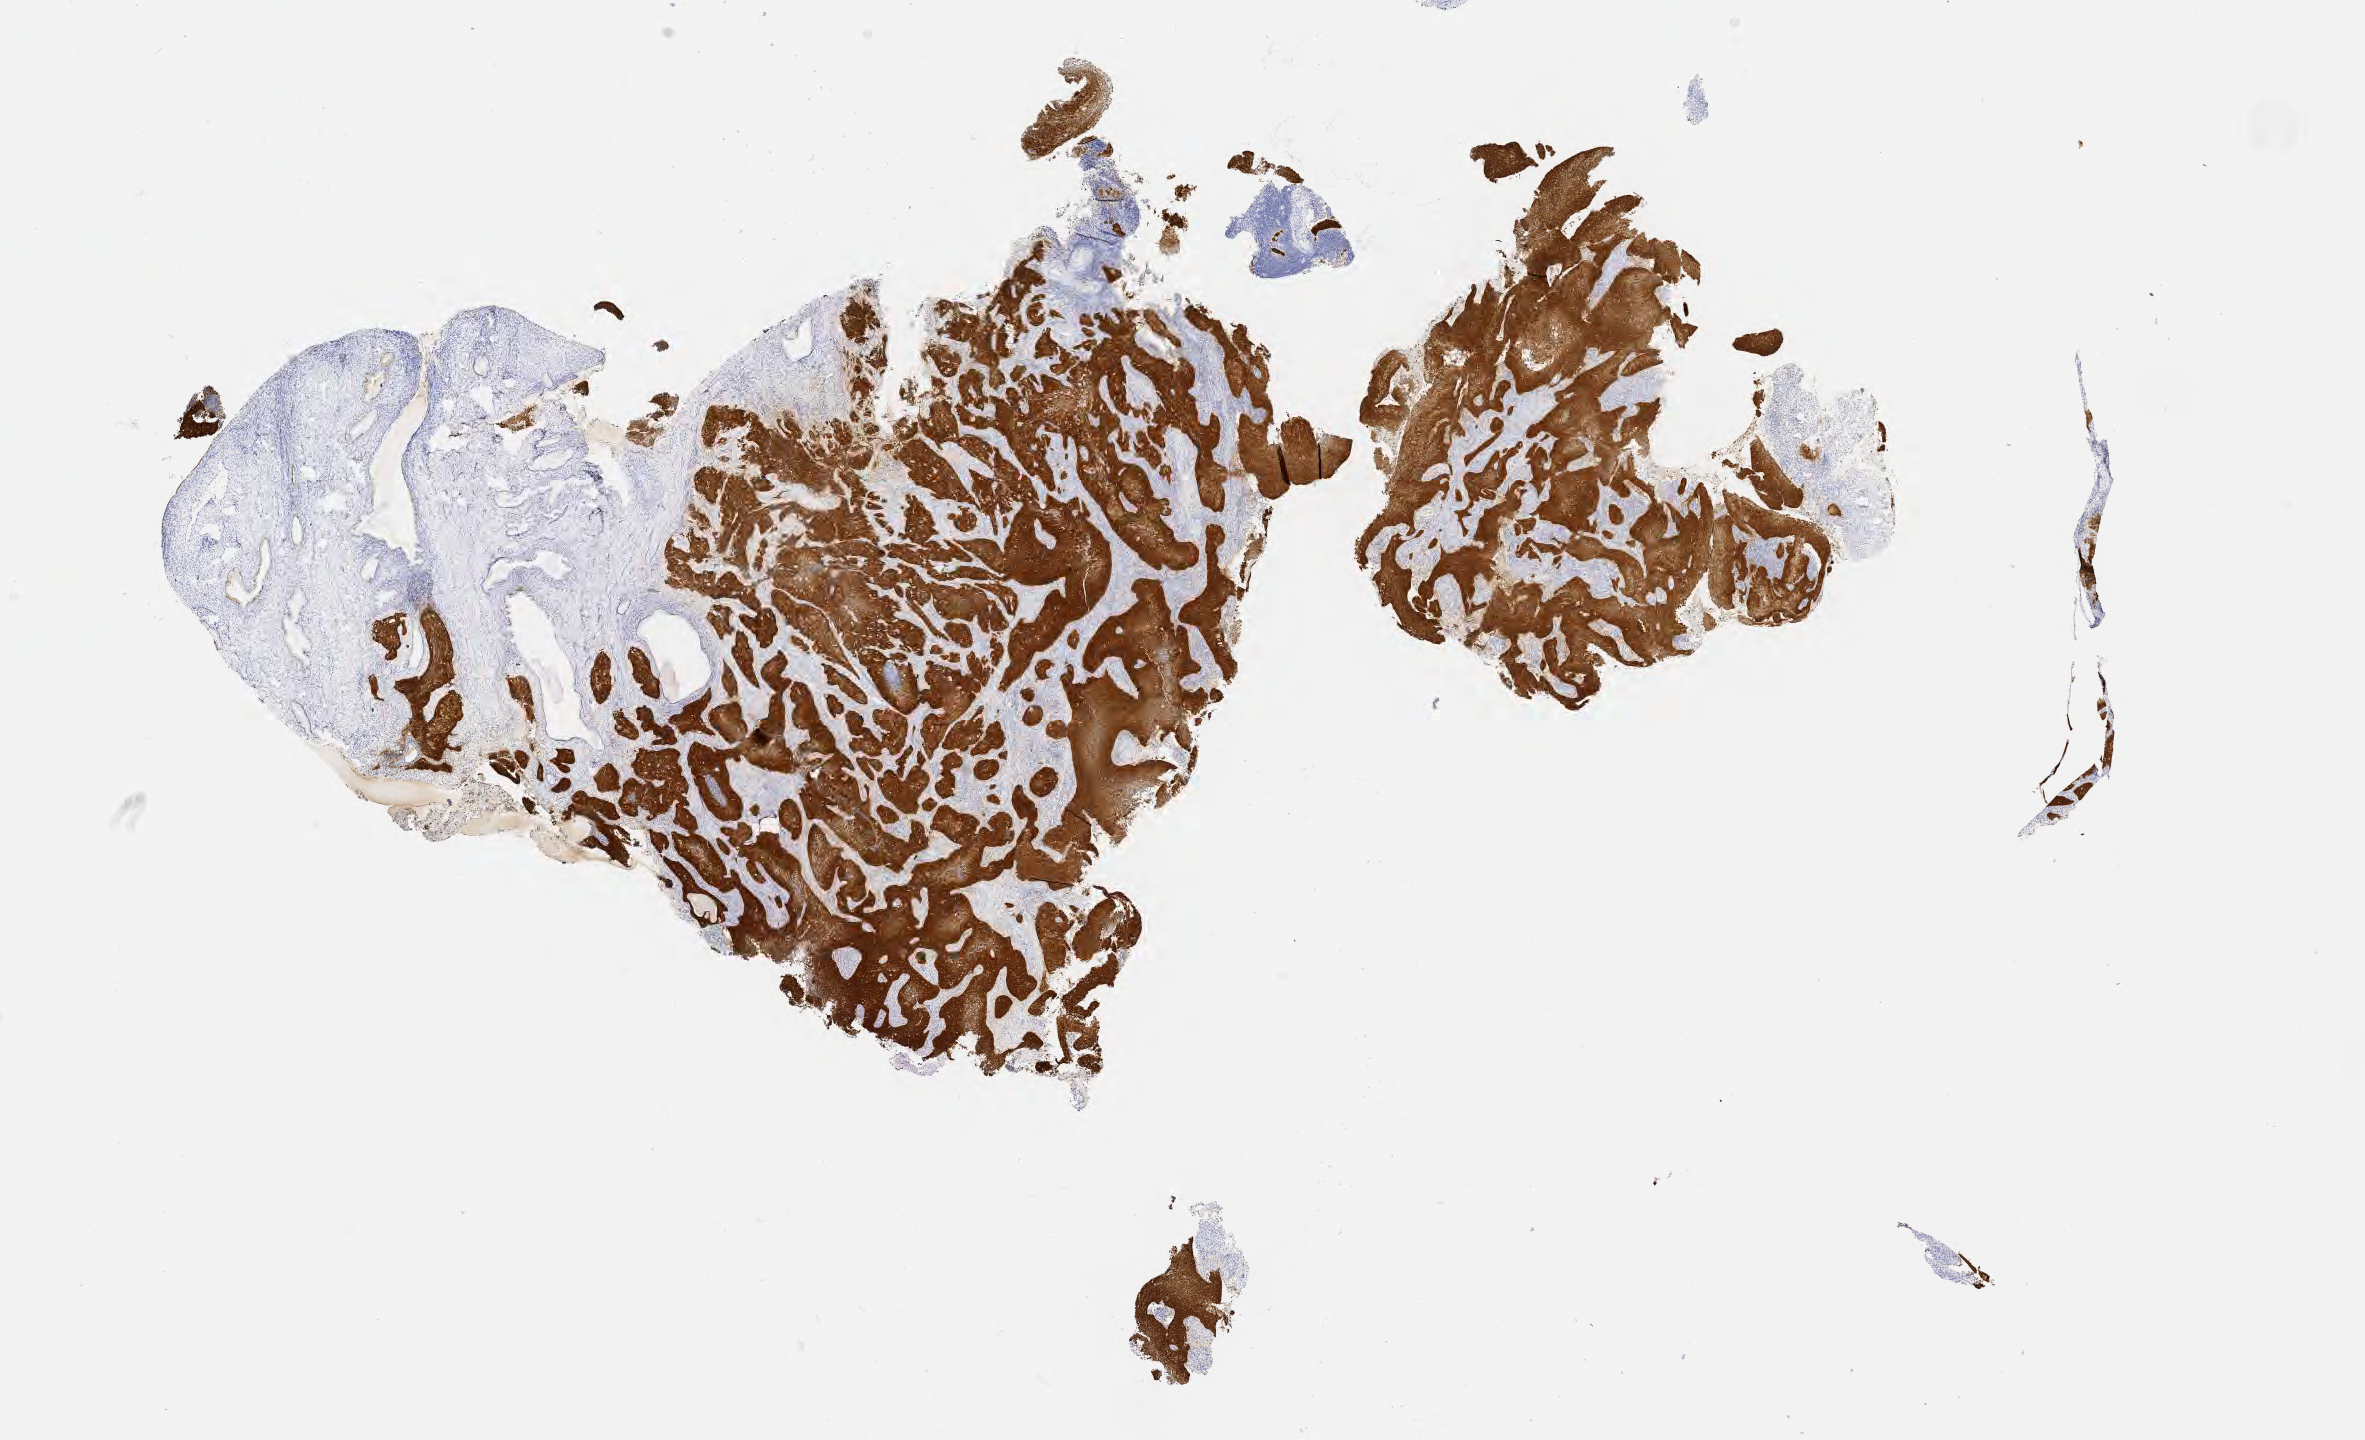
Immunohistochemistry (IHC) whole-slide image stained for p16 (p16INK4a), shown as a low-resolution overview of the whole scanned area (about 19.1 x 11.6 mm). Tumor tissue. Anatomic site: cervix. Patient: female, 50 years old.
Histologic diagnosis: Squamous cell carcinoma, large cell, nonkeratinizing, NOS.